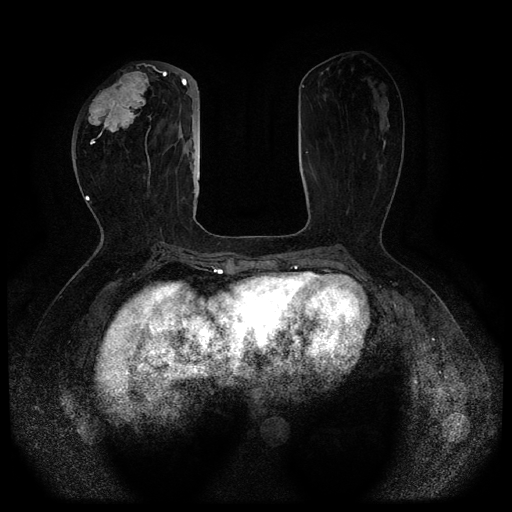
Breast MRI (dynamic contrast-enhanced, multi-phase), one axial slice; position 37 of 116 along the scan axis; dynamic contrast-enhanced series, time point 2 of 5 at this slice position (early post-contrast); 1.5 T; TE 2.6 ms, TR 5.3 ms; 512 × 512 image matrix, field of view 350 × 350 mm. Patient: female, 51 years.
Annotated regions visible in this slice (semi-automatically segmented with operator editing):
- breast lesion (labelled 'tumour' in the annotation; benign lesions carry a separate 'benign' label): bounding box (x1, y1, x2, y2) in pixels: (88, 70, 150, 145)